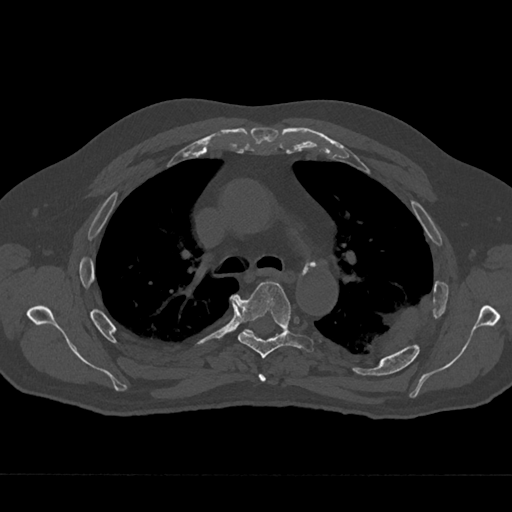
CT including the spine, one axial slice; position 472 of 797 along the scan axis; 120 kVp; bone window (W 1800 / L 400 HU); 0.5 mm slice thickness; 512 × 512 image matrix, field of view 377 × 377 mm. Patient: male, 75 years. From the clinical record (not read from this slice): primary cancer: renal; vertebrae with lytic lesions (as recorded): T4.
Structures marked on this image (semi-automatic segmentation, software-assisted and operator-edited):
- T4 vertebra: bounding box (x1, y1, x2, y2) in pixels: (258, 374, 266, 382)
- T5 vertebra: (236, 281, 314, 358)
- T6 vertebra: (245, 329, 253, 334)